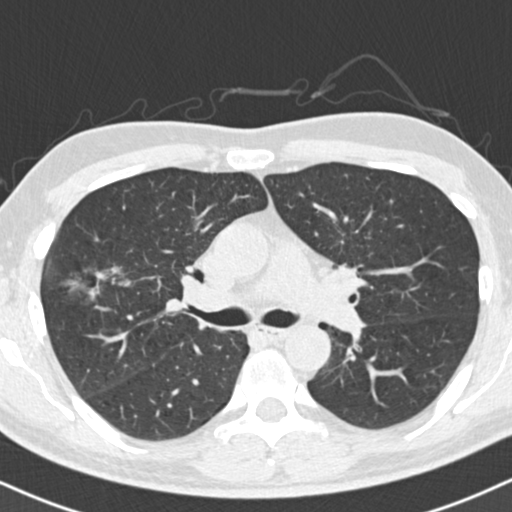
Chest CT (low-dose screening protocol), one axial image; baseline screening round; lung window (W 1500 / L -600 HU); slice 61 of 154 in the series. Male, age 56 years at enrolment.
- Expert reader's lesion annotation, bounding box [x1, y1, x2, y2] px = [53, 253, 143, 318].
- Screening reader's record for this exam: no non-calcified nodule ≥4 mm recorded.
- Participant outcome: lung cancer diagnosed 392 days after this screen — bronchiolo-alveolar adenocarcinoma, NOS, right upper lobe, well differentiated (G1), stage IIB (AJCC 6th edition), 30 mm at pathology.